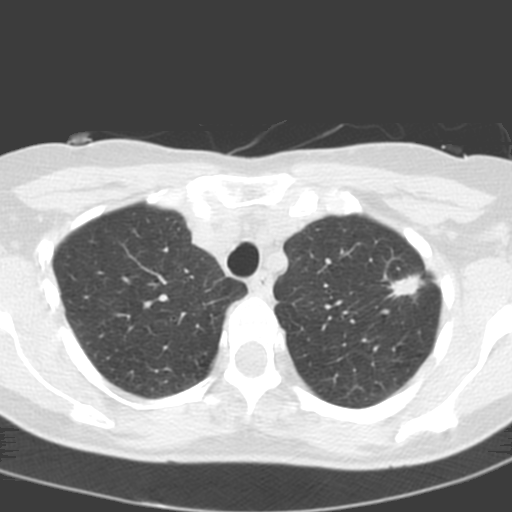
Axial slice from a low-dose chest CT screening exam; baseline screening round; lung window (W 1500 / L -600 HU); 120 kVp; slice 38 of 193 in the series; 512 × 512 image matrix, field of view 272 × 272 mm. Female participant, aged 58 years at enrolment.
- Expert-annotated lung lesion, bounding box <379,265,429,315> (left, top, right, bottom; pixels).
- Reader record for this screening exam (exam-level; its link to the box is not recorded): non-calcified nodule or mass ≥4 mm, left upper lobe, 14 × 10 mm, spiculated (stellate) margins, soft tissue attenuation.
- Official screen result: positive, change unspecified: nodule(s) >= 4 mm or enlarging nodule(s), mass(es), or other non-specific abnormalities suspicious for lung cancer.
- Later outcome: lung cancer diagnosed 48 days after this screen — adenocarcinoma, NOS, left upper lobe, poorly differentiated (G3), stage IA (AJCC 6th edition), 13 mm at pathology.